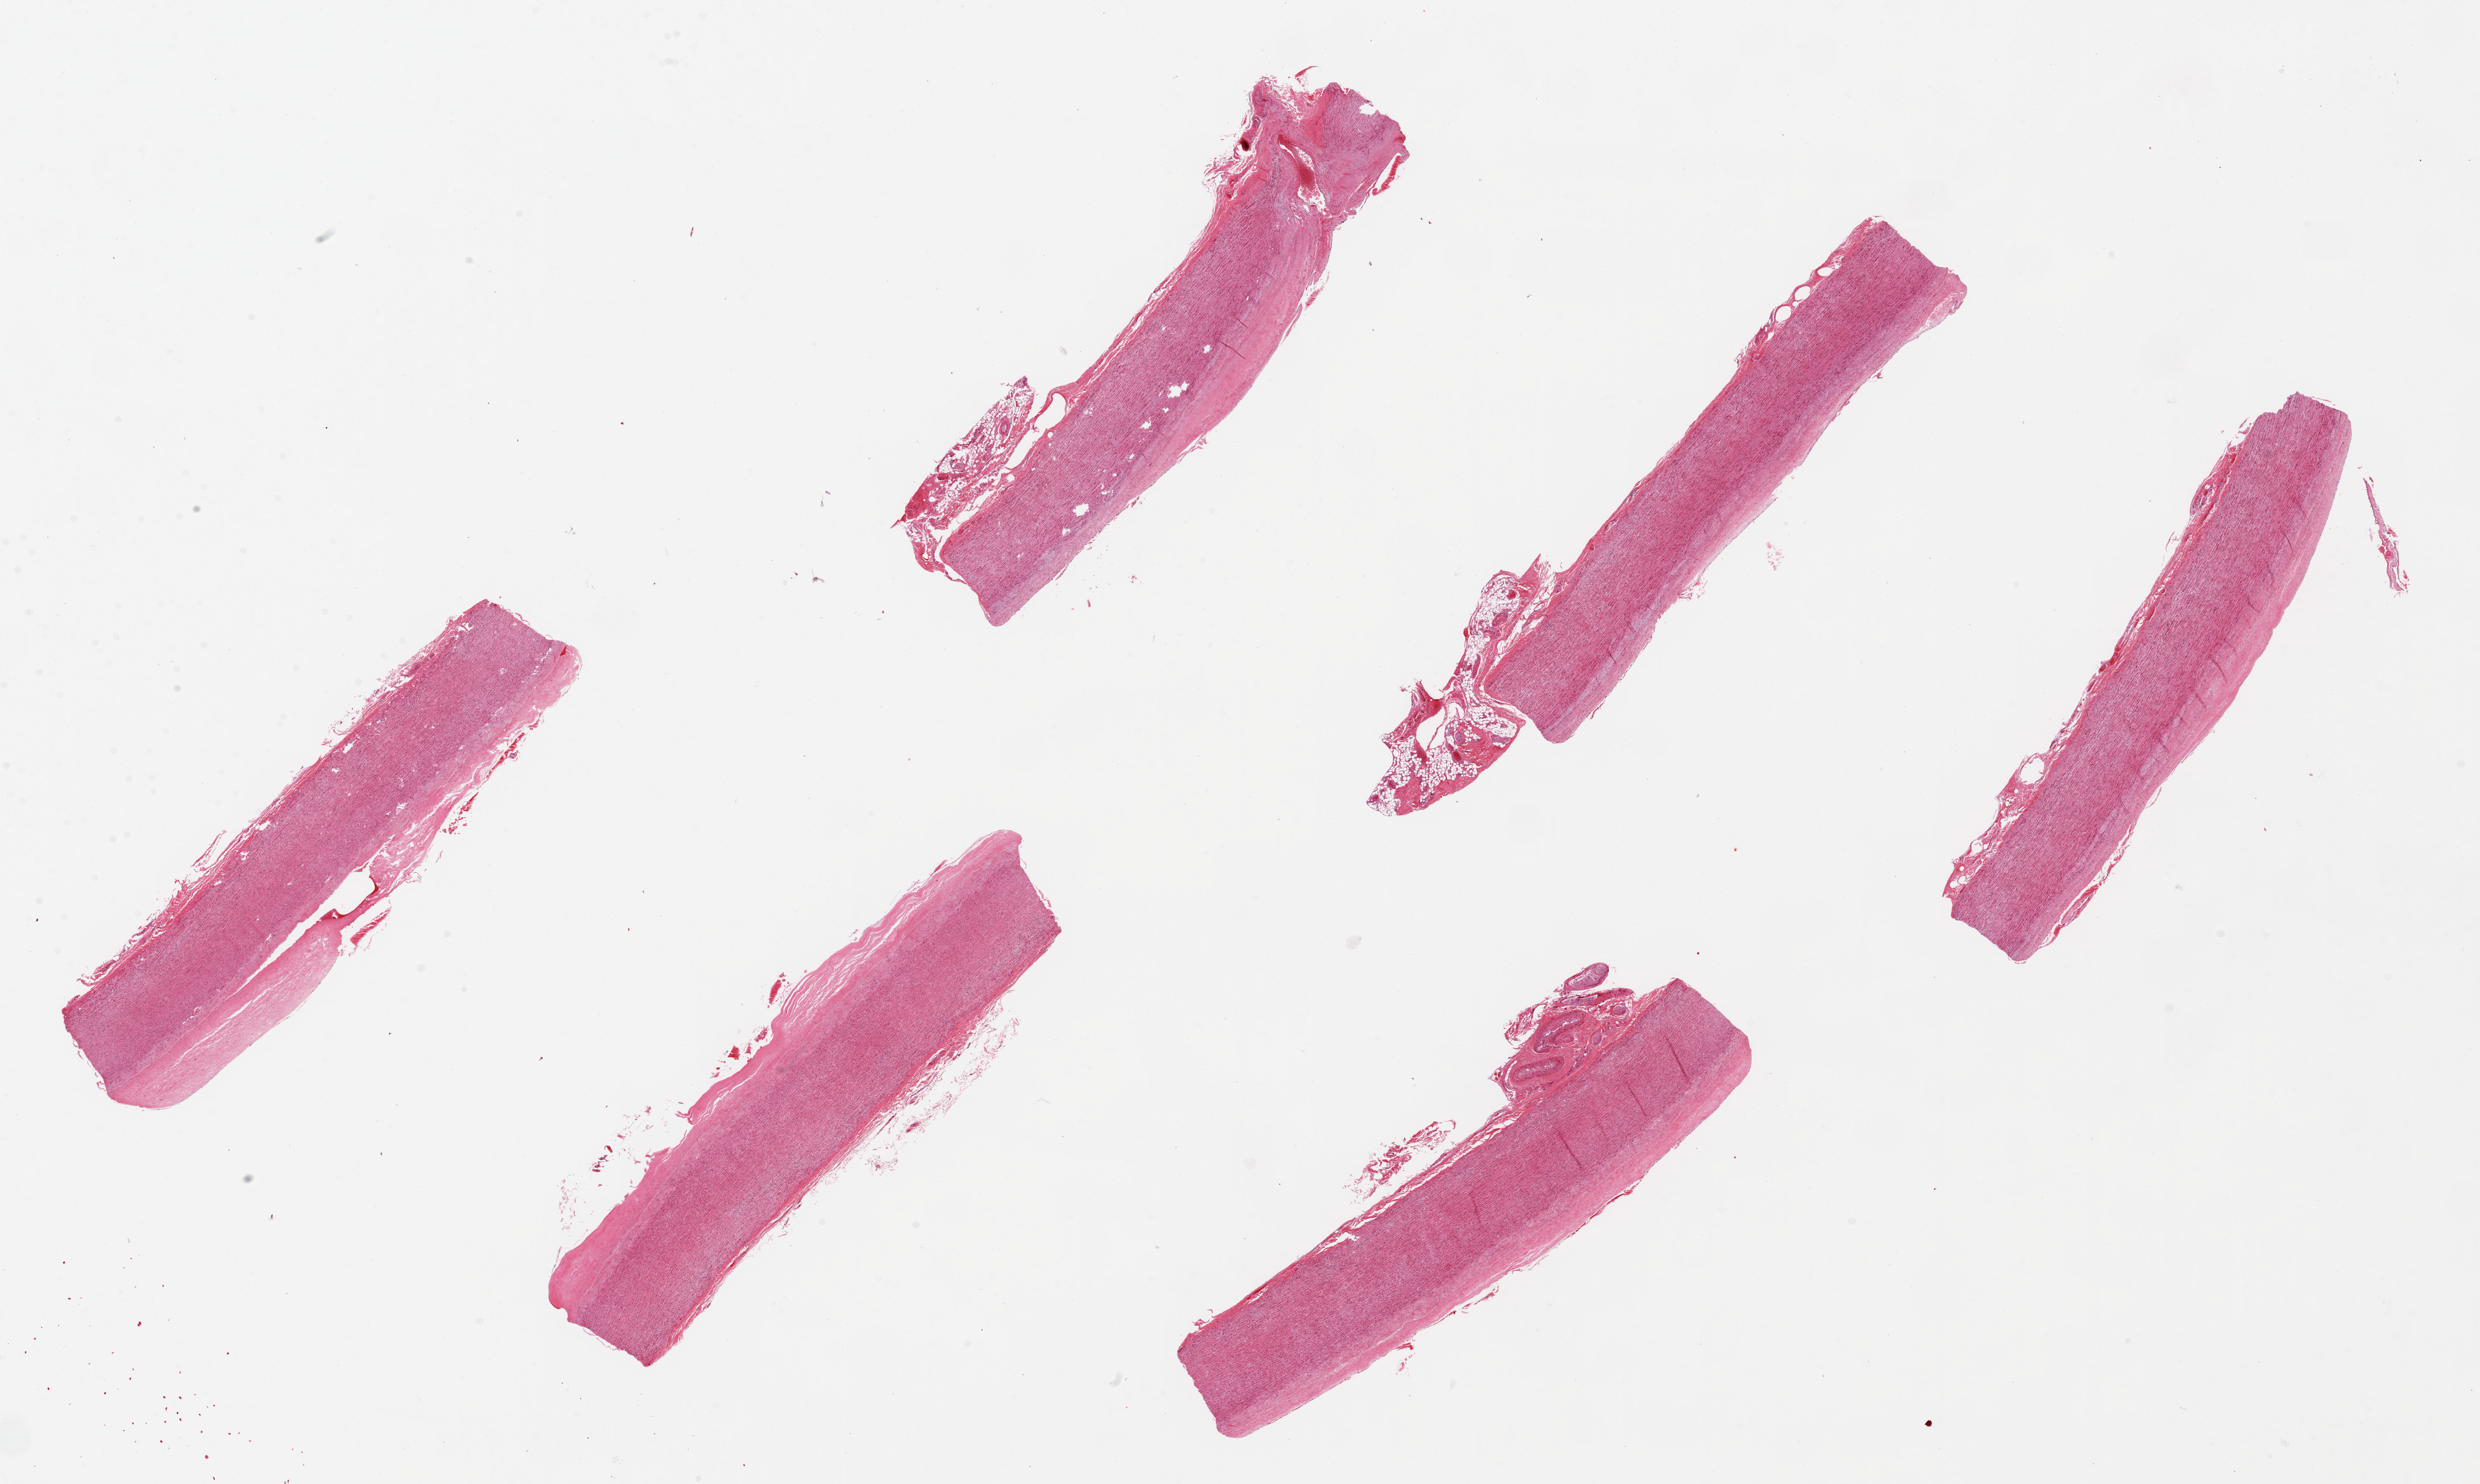
Digitized H&E-stained section, shown as a low-resolution overview of the whole scanned area (about 31.5 x 18.9 mm, acquisition: 20x scan), PAXgene-fixed paraffin-embedded (PFPE) section, target tissue: aorta, donor tissue sample. Donor sex: female.
• reviewer comment on this tissue sample: 6 pieces up to 8x2 mm; minimal plaque